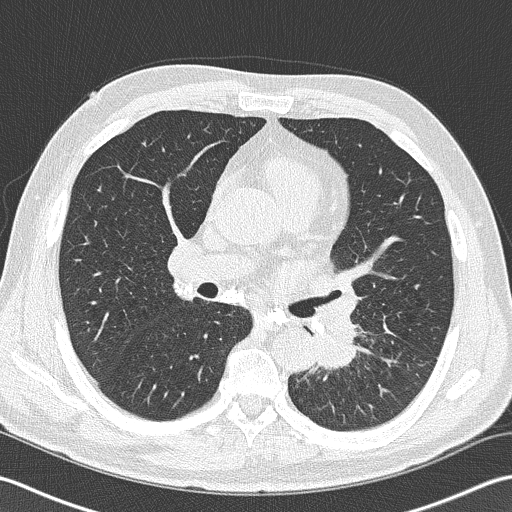
Axial slice from a low-dose chest CT screening exam, second annual screen, lung window (W 1500 / L -600 HU), 2 mm slice thickness, lung (sharp) reconstruction kernel (B50f), slice 73 of 170 in the series, 512 × 512 image matrix. Male, age 57 years at enrolment. Former smoker at enrolment.
Lesion marked by an expert reader, bounding box (x1, y1, x2, y2) in pixels: (293, 303, 373, 382). Screening reader's record for this exam (one nodule recorded; not confirmed to be the boxed lesion): non-calcified nodule or mass ≥4 mm, left lower lobe, 40 × 30 mm, spiculated (stellate) margins, soft tissue attenuation, pre-existing on the prior screen: no. Official screen result: positive, other. Participant outcome: lung cancer diagnosed 9 days after this screen — squamous cell carcinoma, NOS, left lower lobe, moderately differentiated (G2), stage IIIB (AJCC 6th edition), 38 mm at pathology.